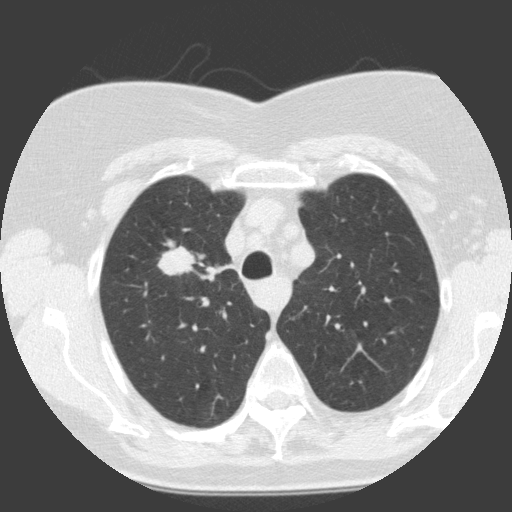
Low-dose screening chest CT, axial slice, first (baseline) screen, lung window (W 1500 / L -600 HU), 2 mm slice thickness, standard (soft-tissue) reconstruction kernel (C), 120 kVp, 512 × 512 image matrix, field of view 300 × 300 mm. Female participant, aged 68 years at enrolment. Current smoker at enrolment.
Expert-annotated lung lesion, box from (x=155, y=238) to (x=204, y=284) px. Screening reader's record for this exam (one nodule recorded; not confirmed to be the boxed lesion): non-calcified nodule or mass ≥4 mm, right upper lobe, 19 × 12 mm, smooth margins, soft tissue attenuation. Participant outcome: lung cancer diagnosed 30 days after this screen — squamous cell carcinoma, NOS, right upper lobe, moderately differentiated (G2), stage IA (AJCC 6th edition), 28 mm at pathology.